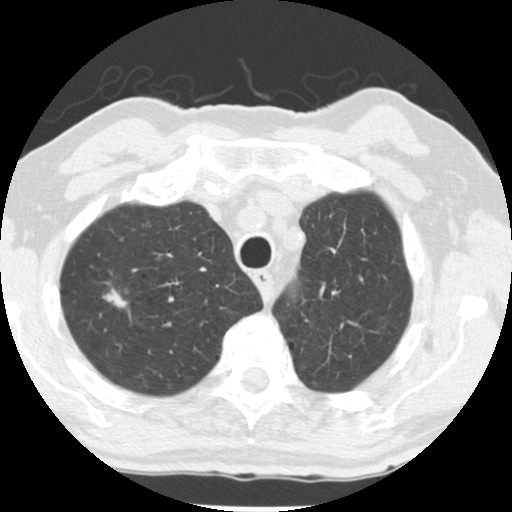
Low-dose screening chest CT, axial slice. First (baseline) screen. Lung window (W 1500 / L -600 HU). 2.5 mm slice thickness. Standard (soft-tissue) reconstruction kernel (STANDARD). 120 kVp. Slice 208 of 252 in the series. Male, age 69 years at enrolment.
Expert reader's lesion annotation, bounding box [x1, y1, x2, y2] px = [89, 271, 146, 330]. The screening reader recorded 2 non-calcified nodules or masses ≥4 mm on this exam; which of them this box marks is not recorded. Official screen result: positive, change unspecified: nodule(s) >= 4 mm or enlarging nodule(s), mass(es), or other non-specific abnormalities suspicious for lung cancer. Participant outcome: lung cancer diagnosed 105 days after this screen — adenocarcinoma, NOS, right upper lobe, well differentiated (G1), stage IA (AJCC 6th edition), 17 mm at pathology.